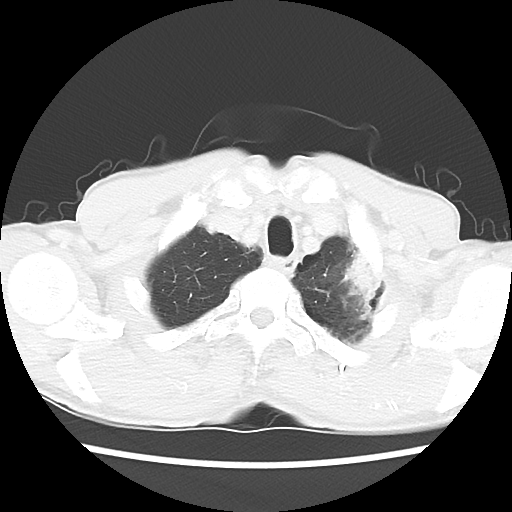
Chest CT, one axial slice. Position 54 of 60 along the scan axis. Reconstruction kernel LUNG. Lung window (W 1500 / L -600 HU). 5 mm slice thickness. 512 × 512 image matrix, field of view 308 × 308 mm. Patient: male, 64 years. Case-level facts recorded for this patient, not image findings: clinical TNM (as recorded): T3 N3 M0.
Annotated regions visible in this slice (bounding box drawn by a radiologist):
- lung tumour (recorded histology: adenocarcinoma): bounding box [x1, y1, x2, y2] px = [340, 244, 384, 307]